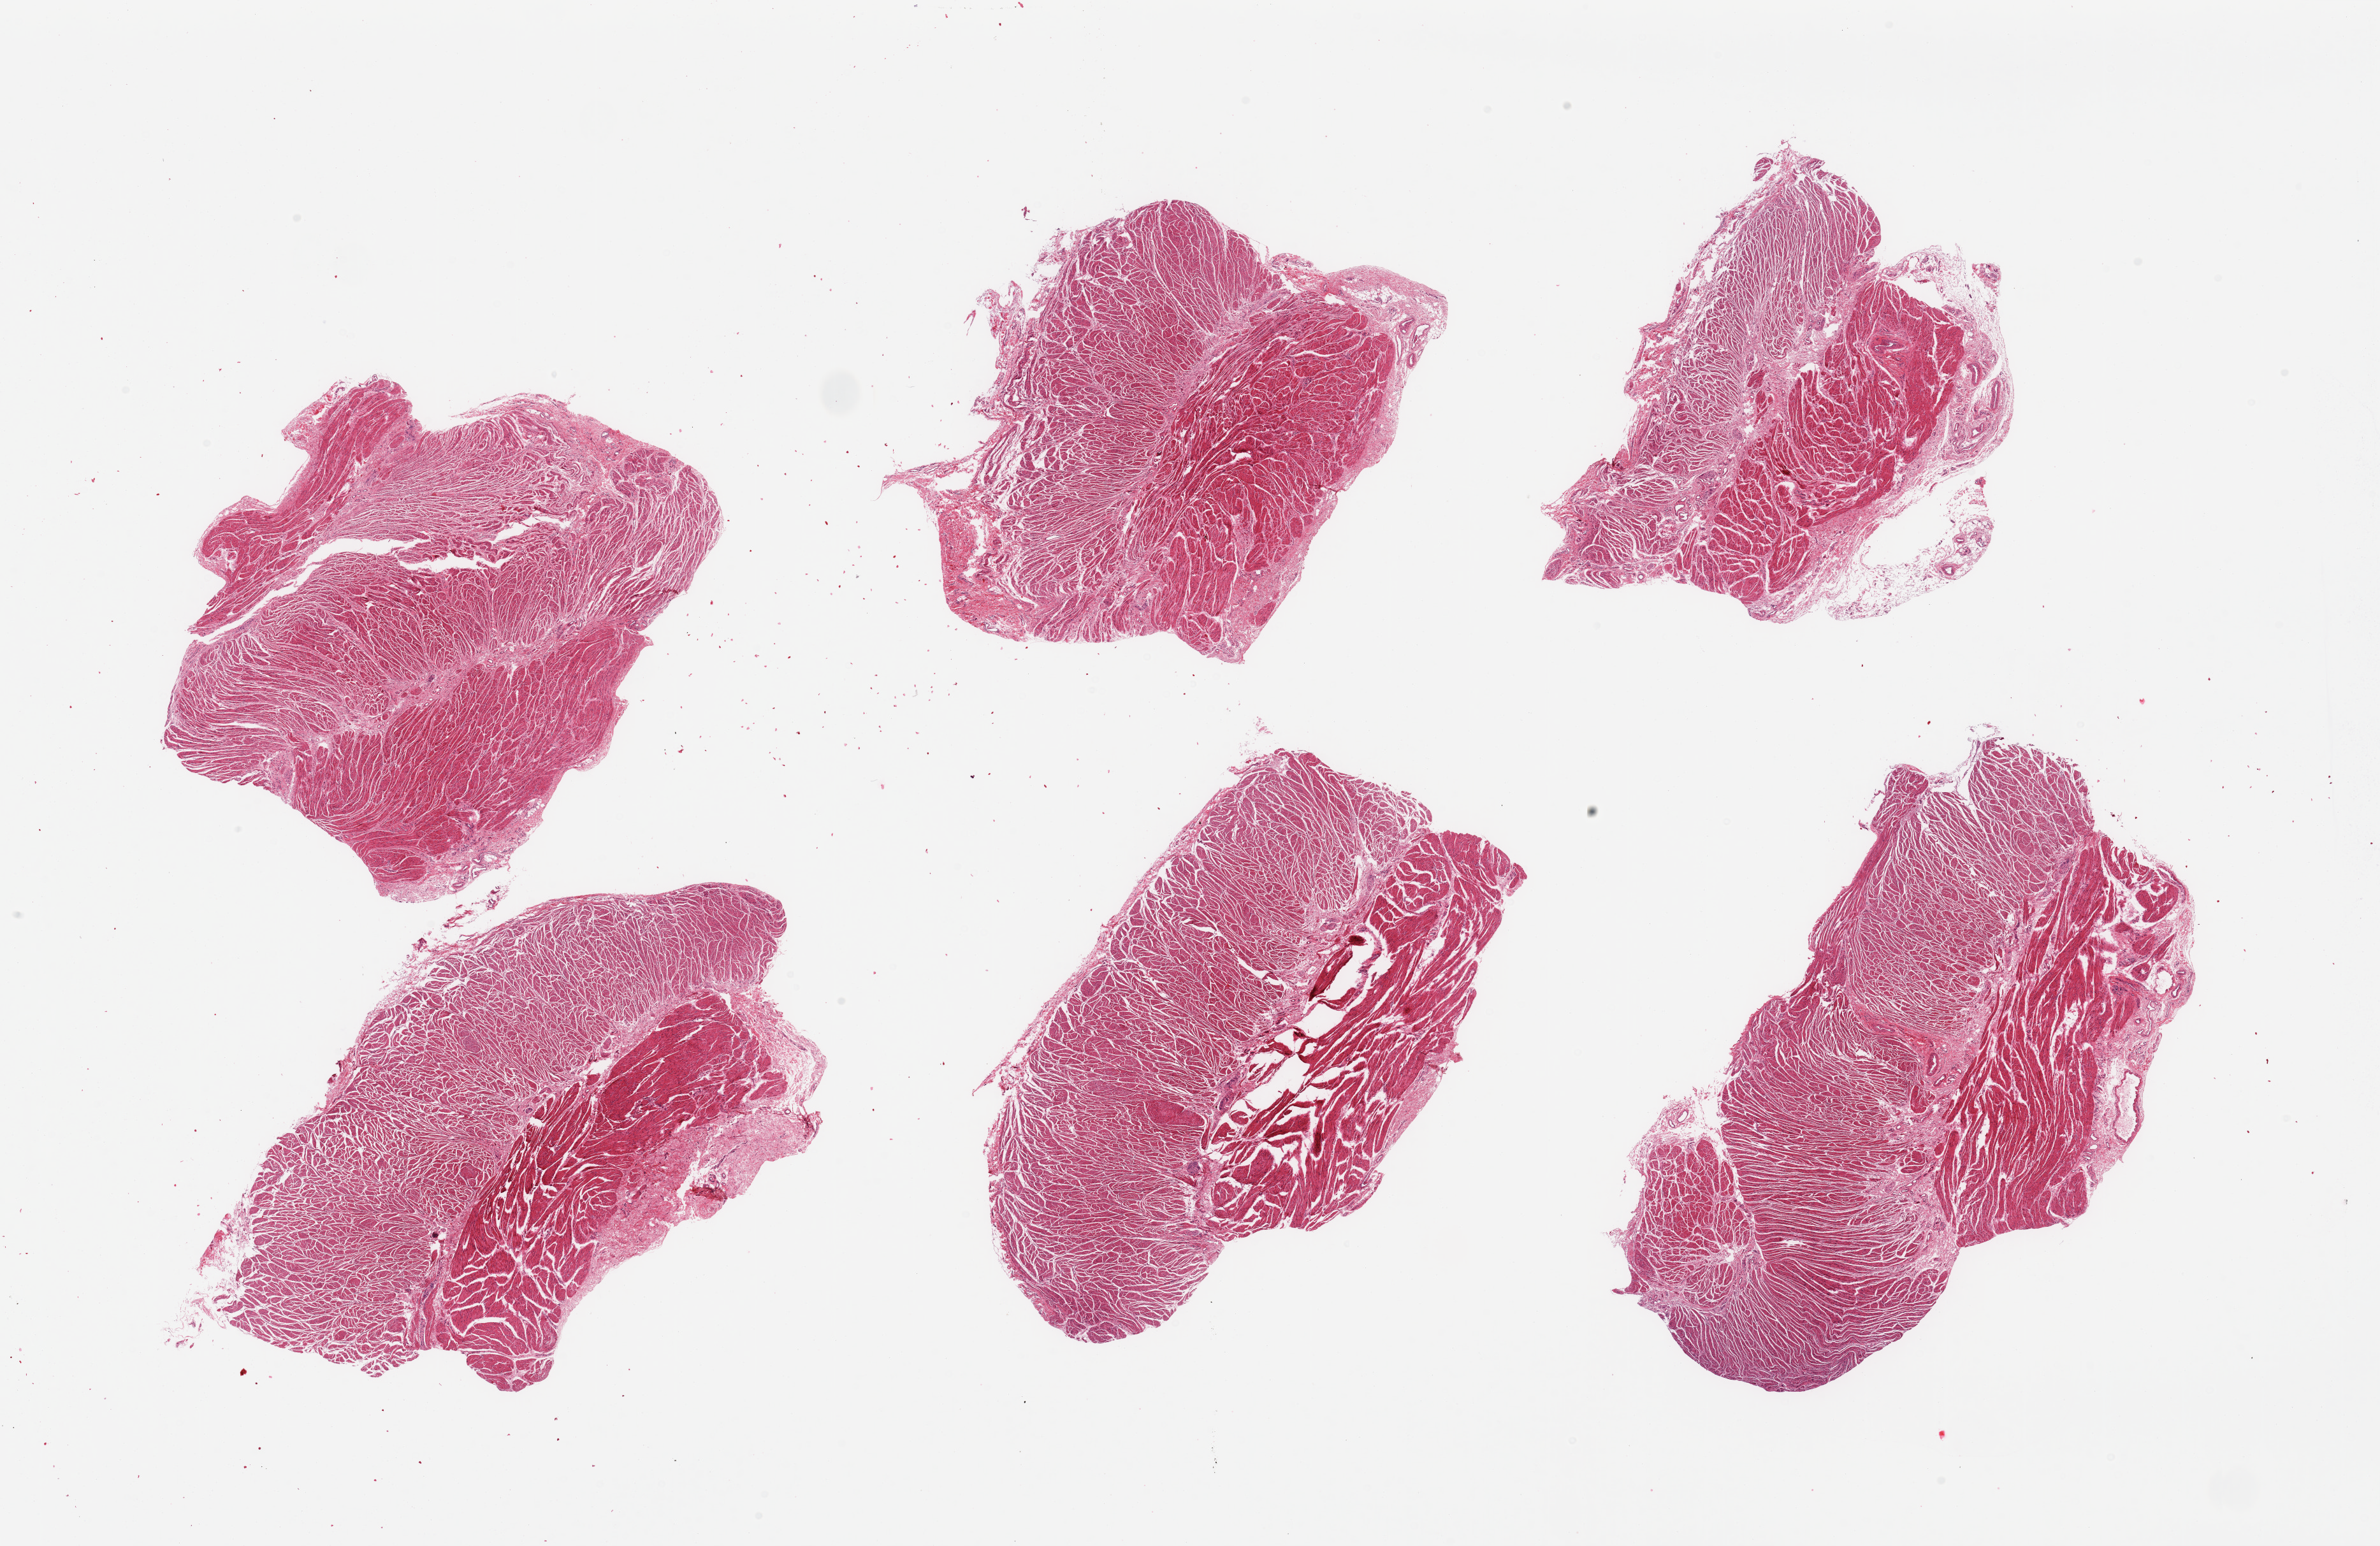
Digitized hematoxylin and eosin (H&E)-stained section, shown as a low-resolution overview of the whole scanned area (about 29.5 x 19.2 mm, from a 20x scan). PAXgene-fixed paraffin-embedded (PFPE) section. Section of gastroesophageal junction (target tissue). Donor tissue sample.
Reviewer comment on this tissue sample: 6 pieces, confirmed target muscularis.